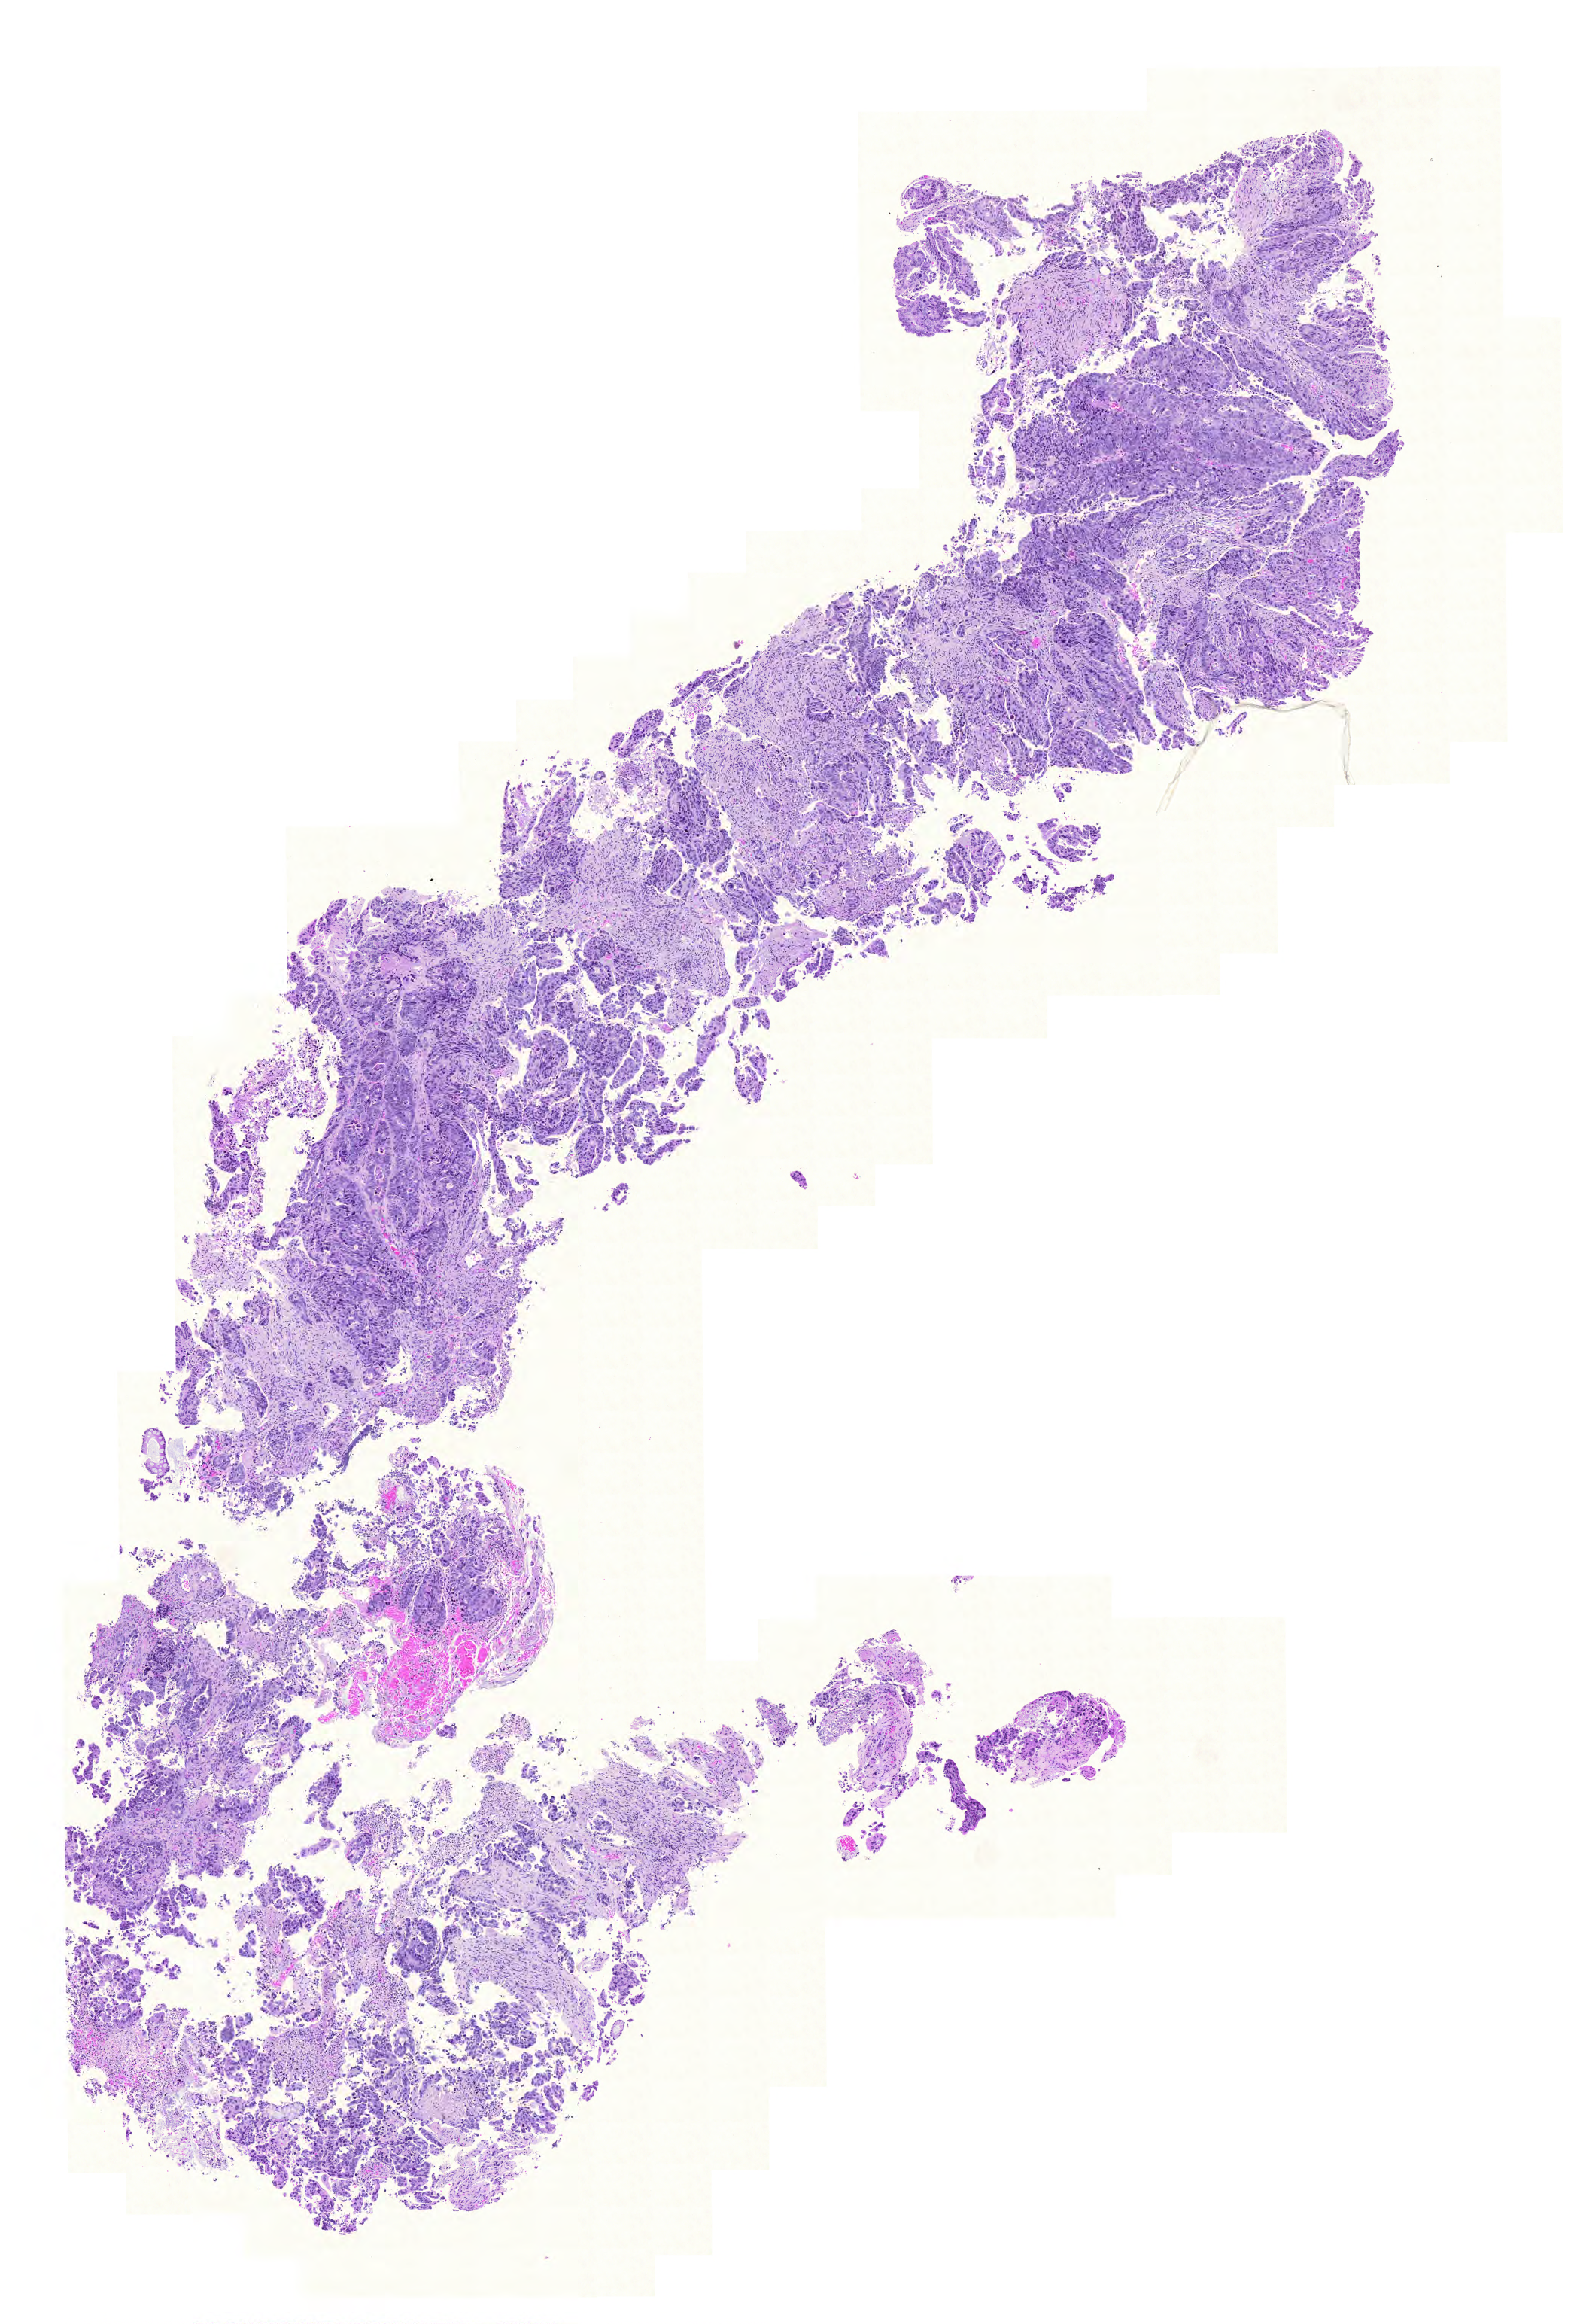
Hematoxylin and eosin (H&E) stained whole-slide image — low-resolution overview of the scanned area, about 7.8 x 11.5 mm, formalin-fixed paraffin-embedded (FFPE) diagnostic section, sample: primary tumour, colon. Male patient; age at initial diagnosis 45 years.
Histologic diagnosis: Adenocarcinoma, NOS. Lymph nodes positive (case pathology): 23 of 29 examined. AJCC pathologic stage: IV.